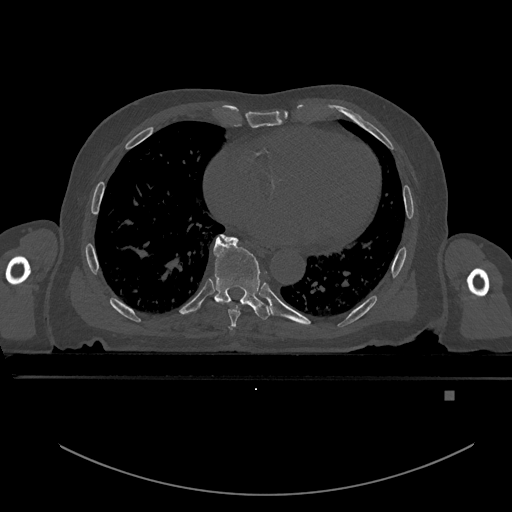
CT including the spine, one axial slice; position 221 of 969 along the scan axis; bone window (W 1800 / L 400 HU); 512 × 512 image matrix, field of view 456 × 456 mm. Patient: male, 82 years. From the clinical record (not read from this slice): primary cancer: prostate; vertebrae with lytic lesions (as recorded): T11, T9, T8, T2.
Annotated regions visible in this slice (semi-automatic segmentation, software-assisted and operator-edited):
- T6 vertebra: bounding box <229,327,232,331> (left, top, right, bottom; pixels)
- T7 vertebra: <222,235,240,326>
- T8 vertebra: <213,236,272,320>